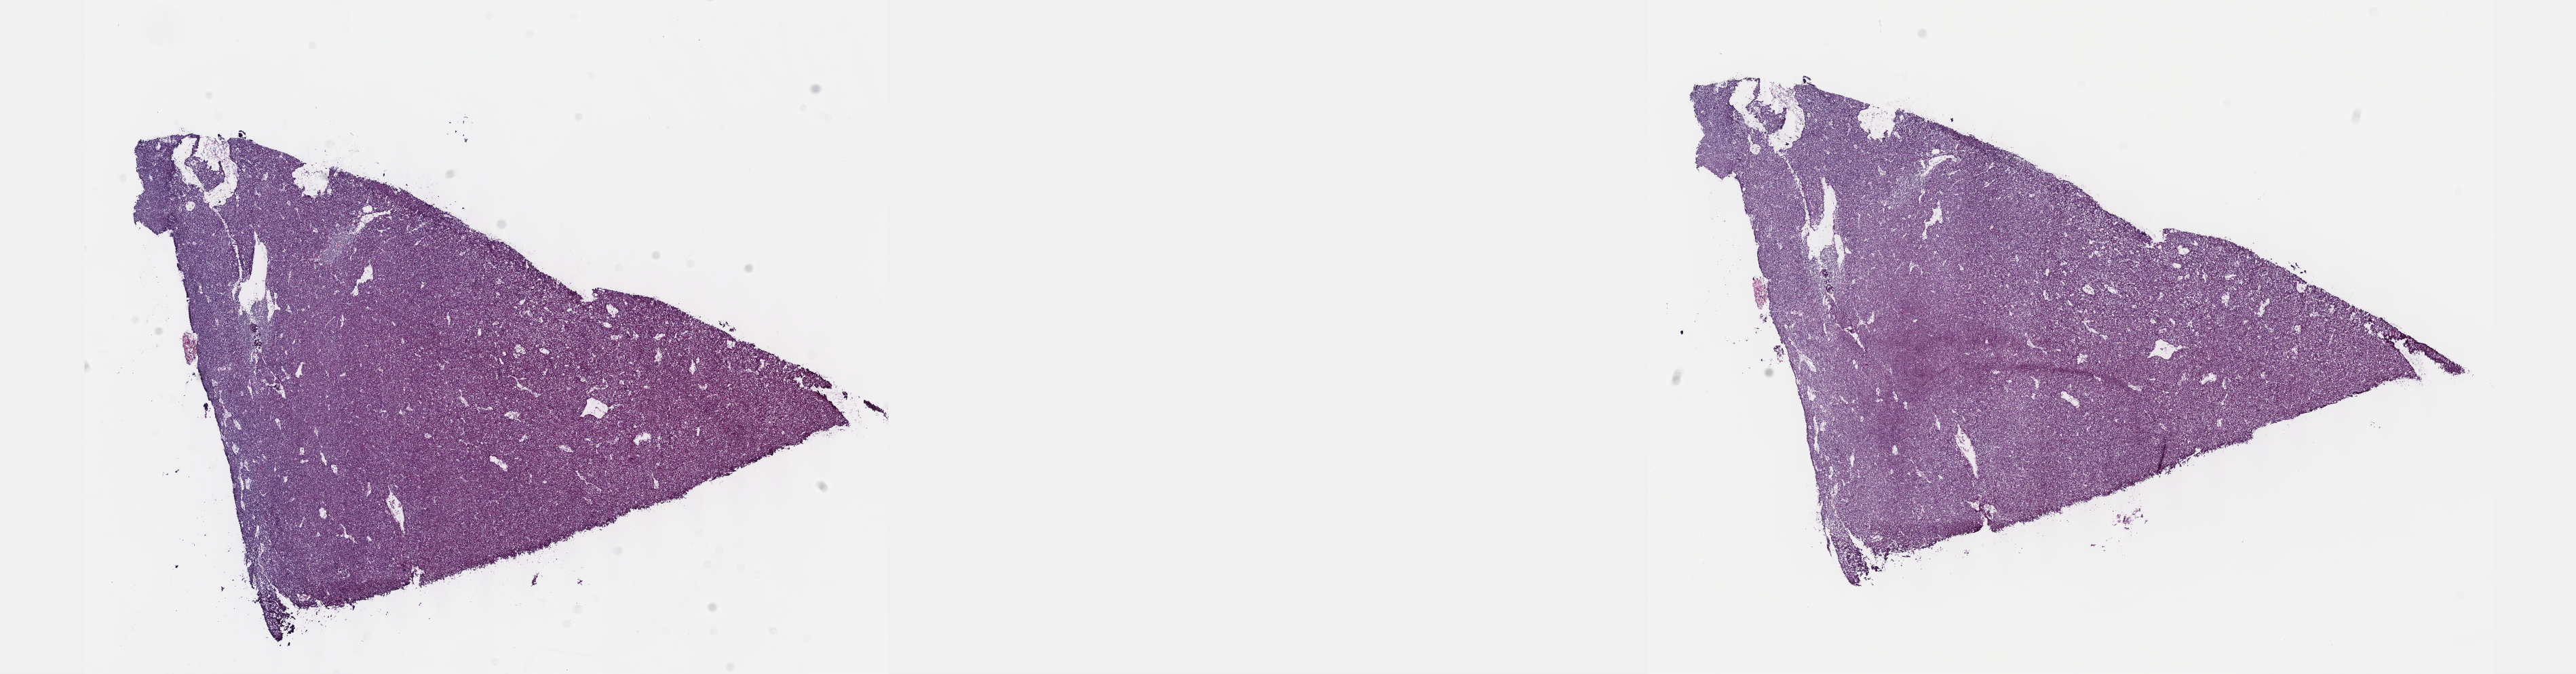
Digitized H&E tissue section (whole slide), shown as a low-resolution overview of the whole scanned area (about 30.7 x 8.0 mm). Frozen section from the top of the tissue portion. Thymus, primary tumour sample. Female, age 84 years at initial diagnosis. Composition of this section per pathologist review: tumour cells 100%, tumour nuclei 80%, normal cells 0%, stromal cells 0%, necrosis 0%. Infiltration values recorded for this section: lymphocyte infiltration 1%, monocyte infiltration 0%, neutrophil infiltration 0%.
Pathologic diagnosis: Thymoma, type A, malignant (anterior mediastinum).